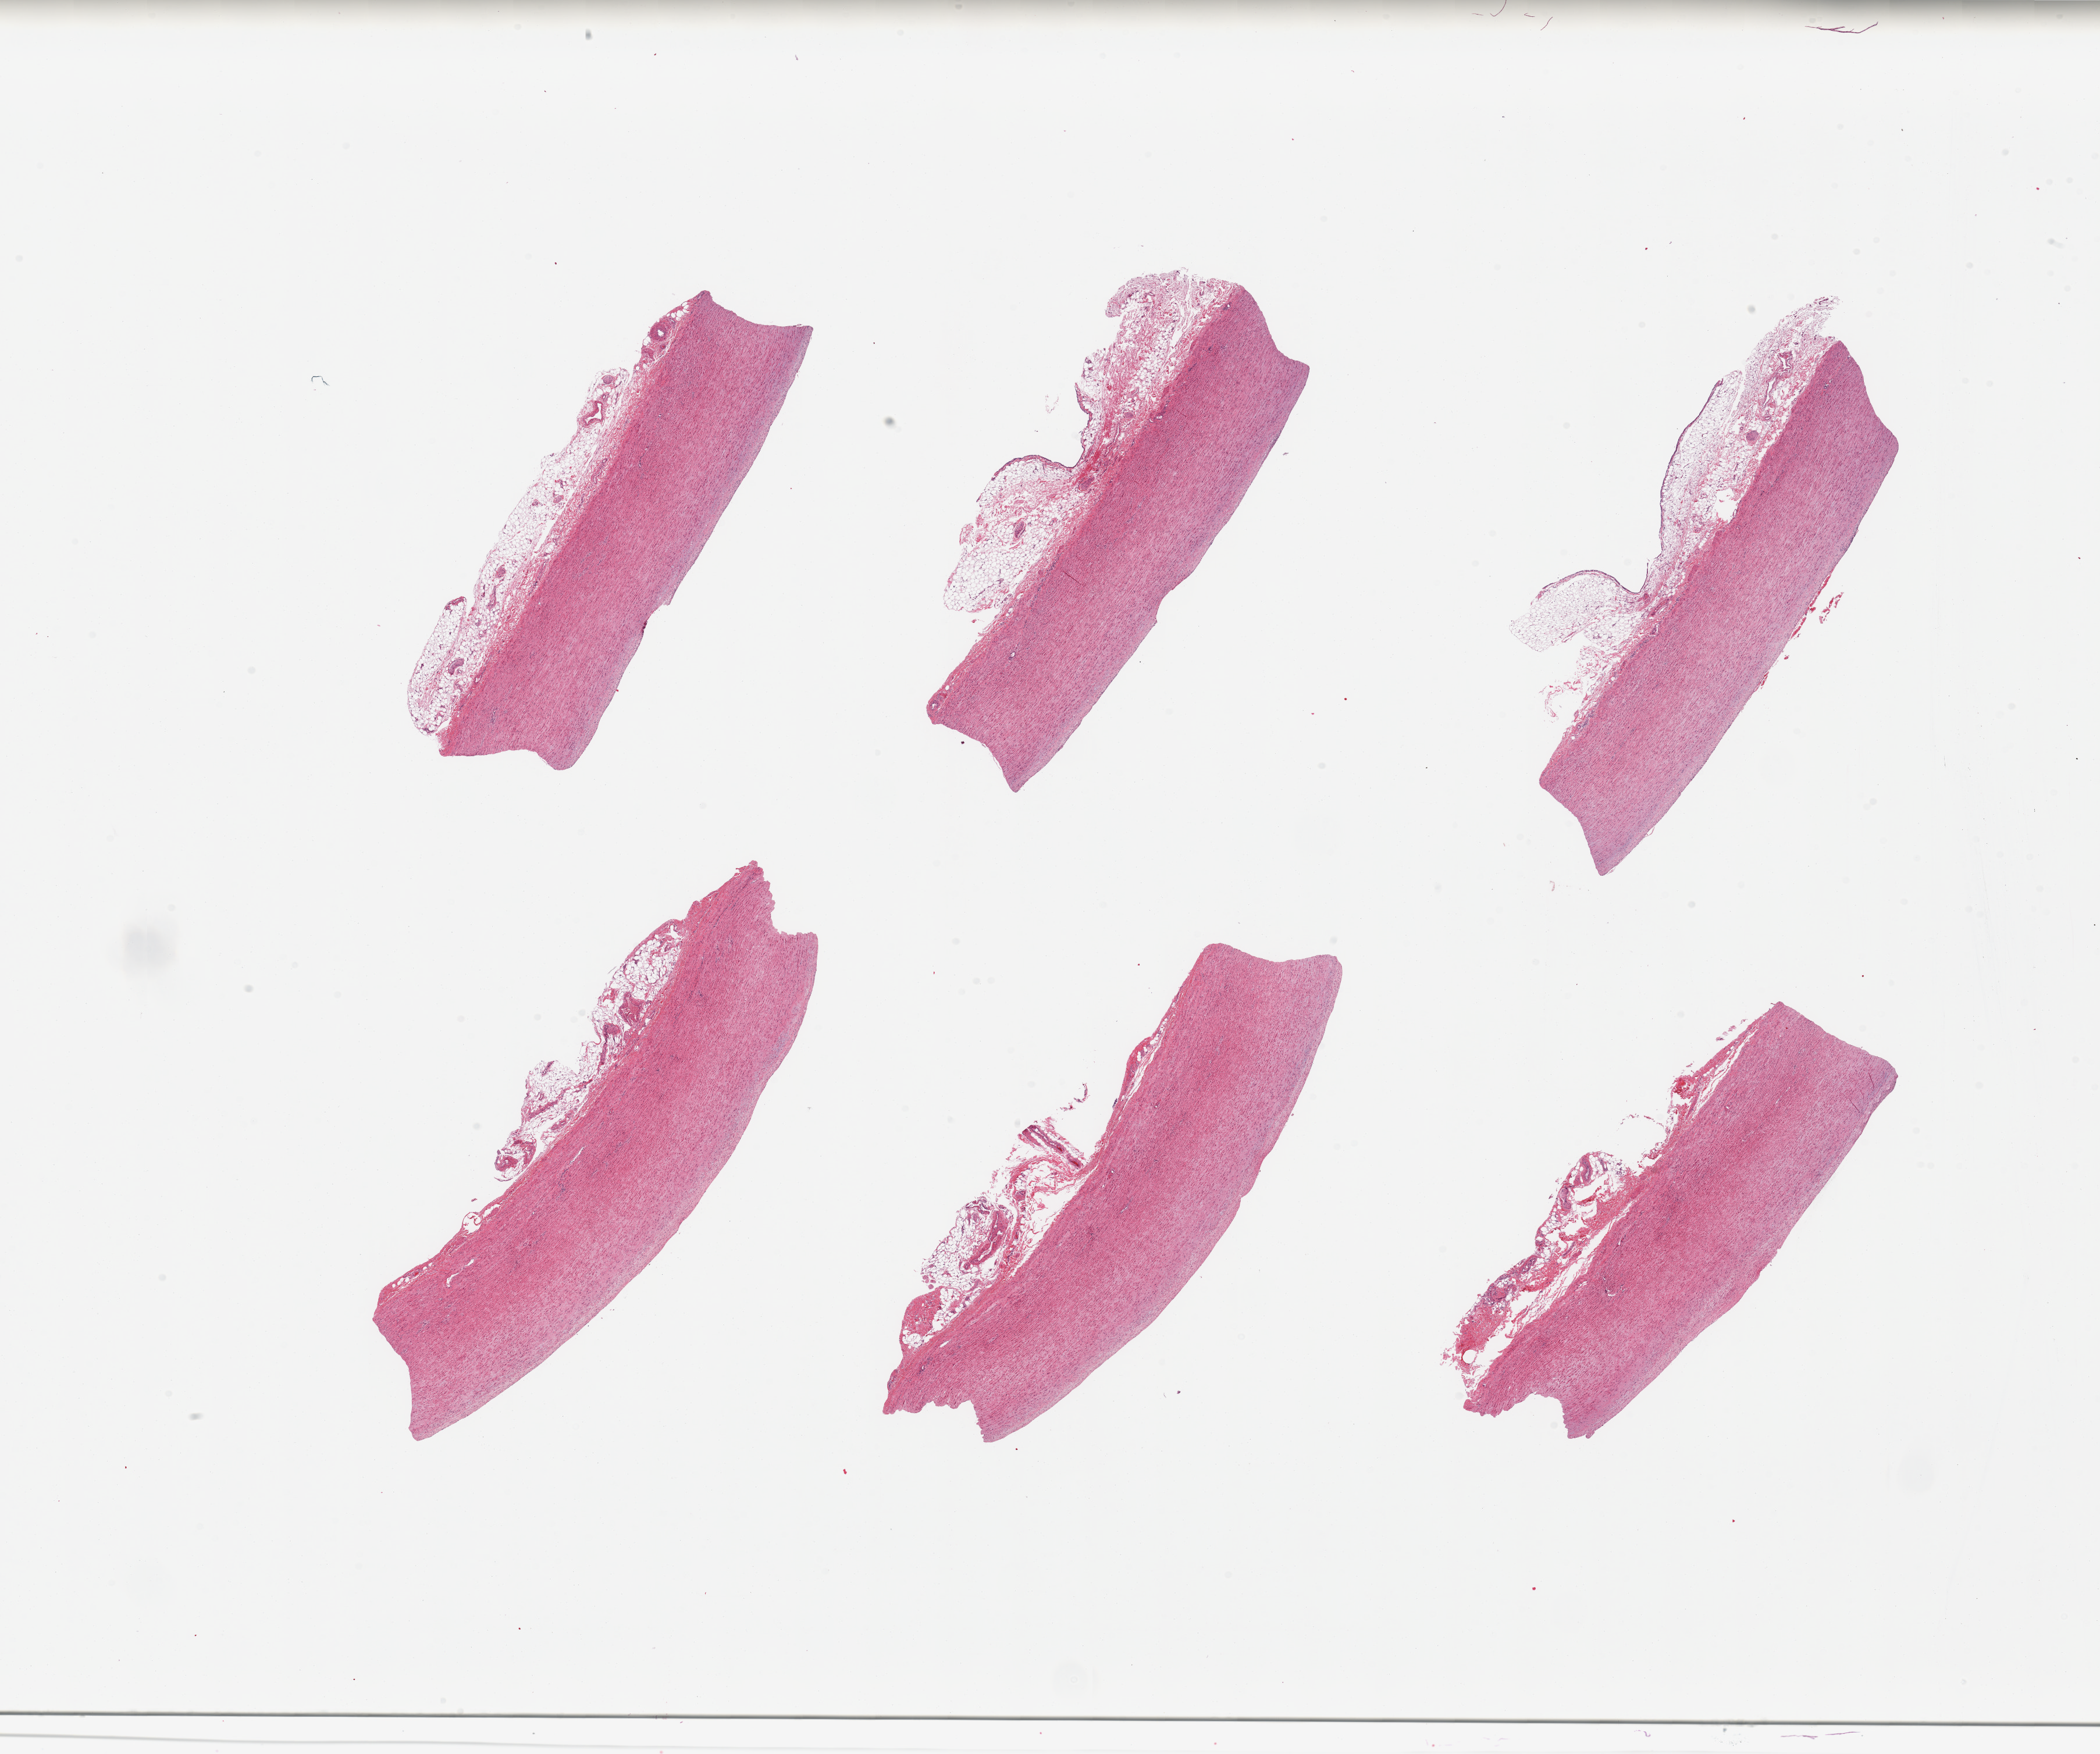
Digitized haematoxylin and eosin-stained section — shown as a low-resolution overview of the whole scanned area (about 28.5 x 23.9 mm, acquisition: 20x scan); PAXgene-fixed paraffin-embedded (PFPE) section; sampled site (target tissue): aorta; donor tissue sample. Male donor.
• reviewer comment on this tissue sample: 6 pieces; several include >1mm adventitia/fat/vasa vasorum, mild atherosclerosis